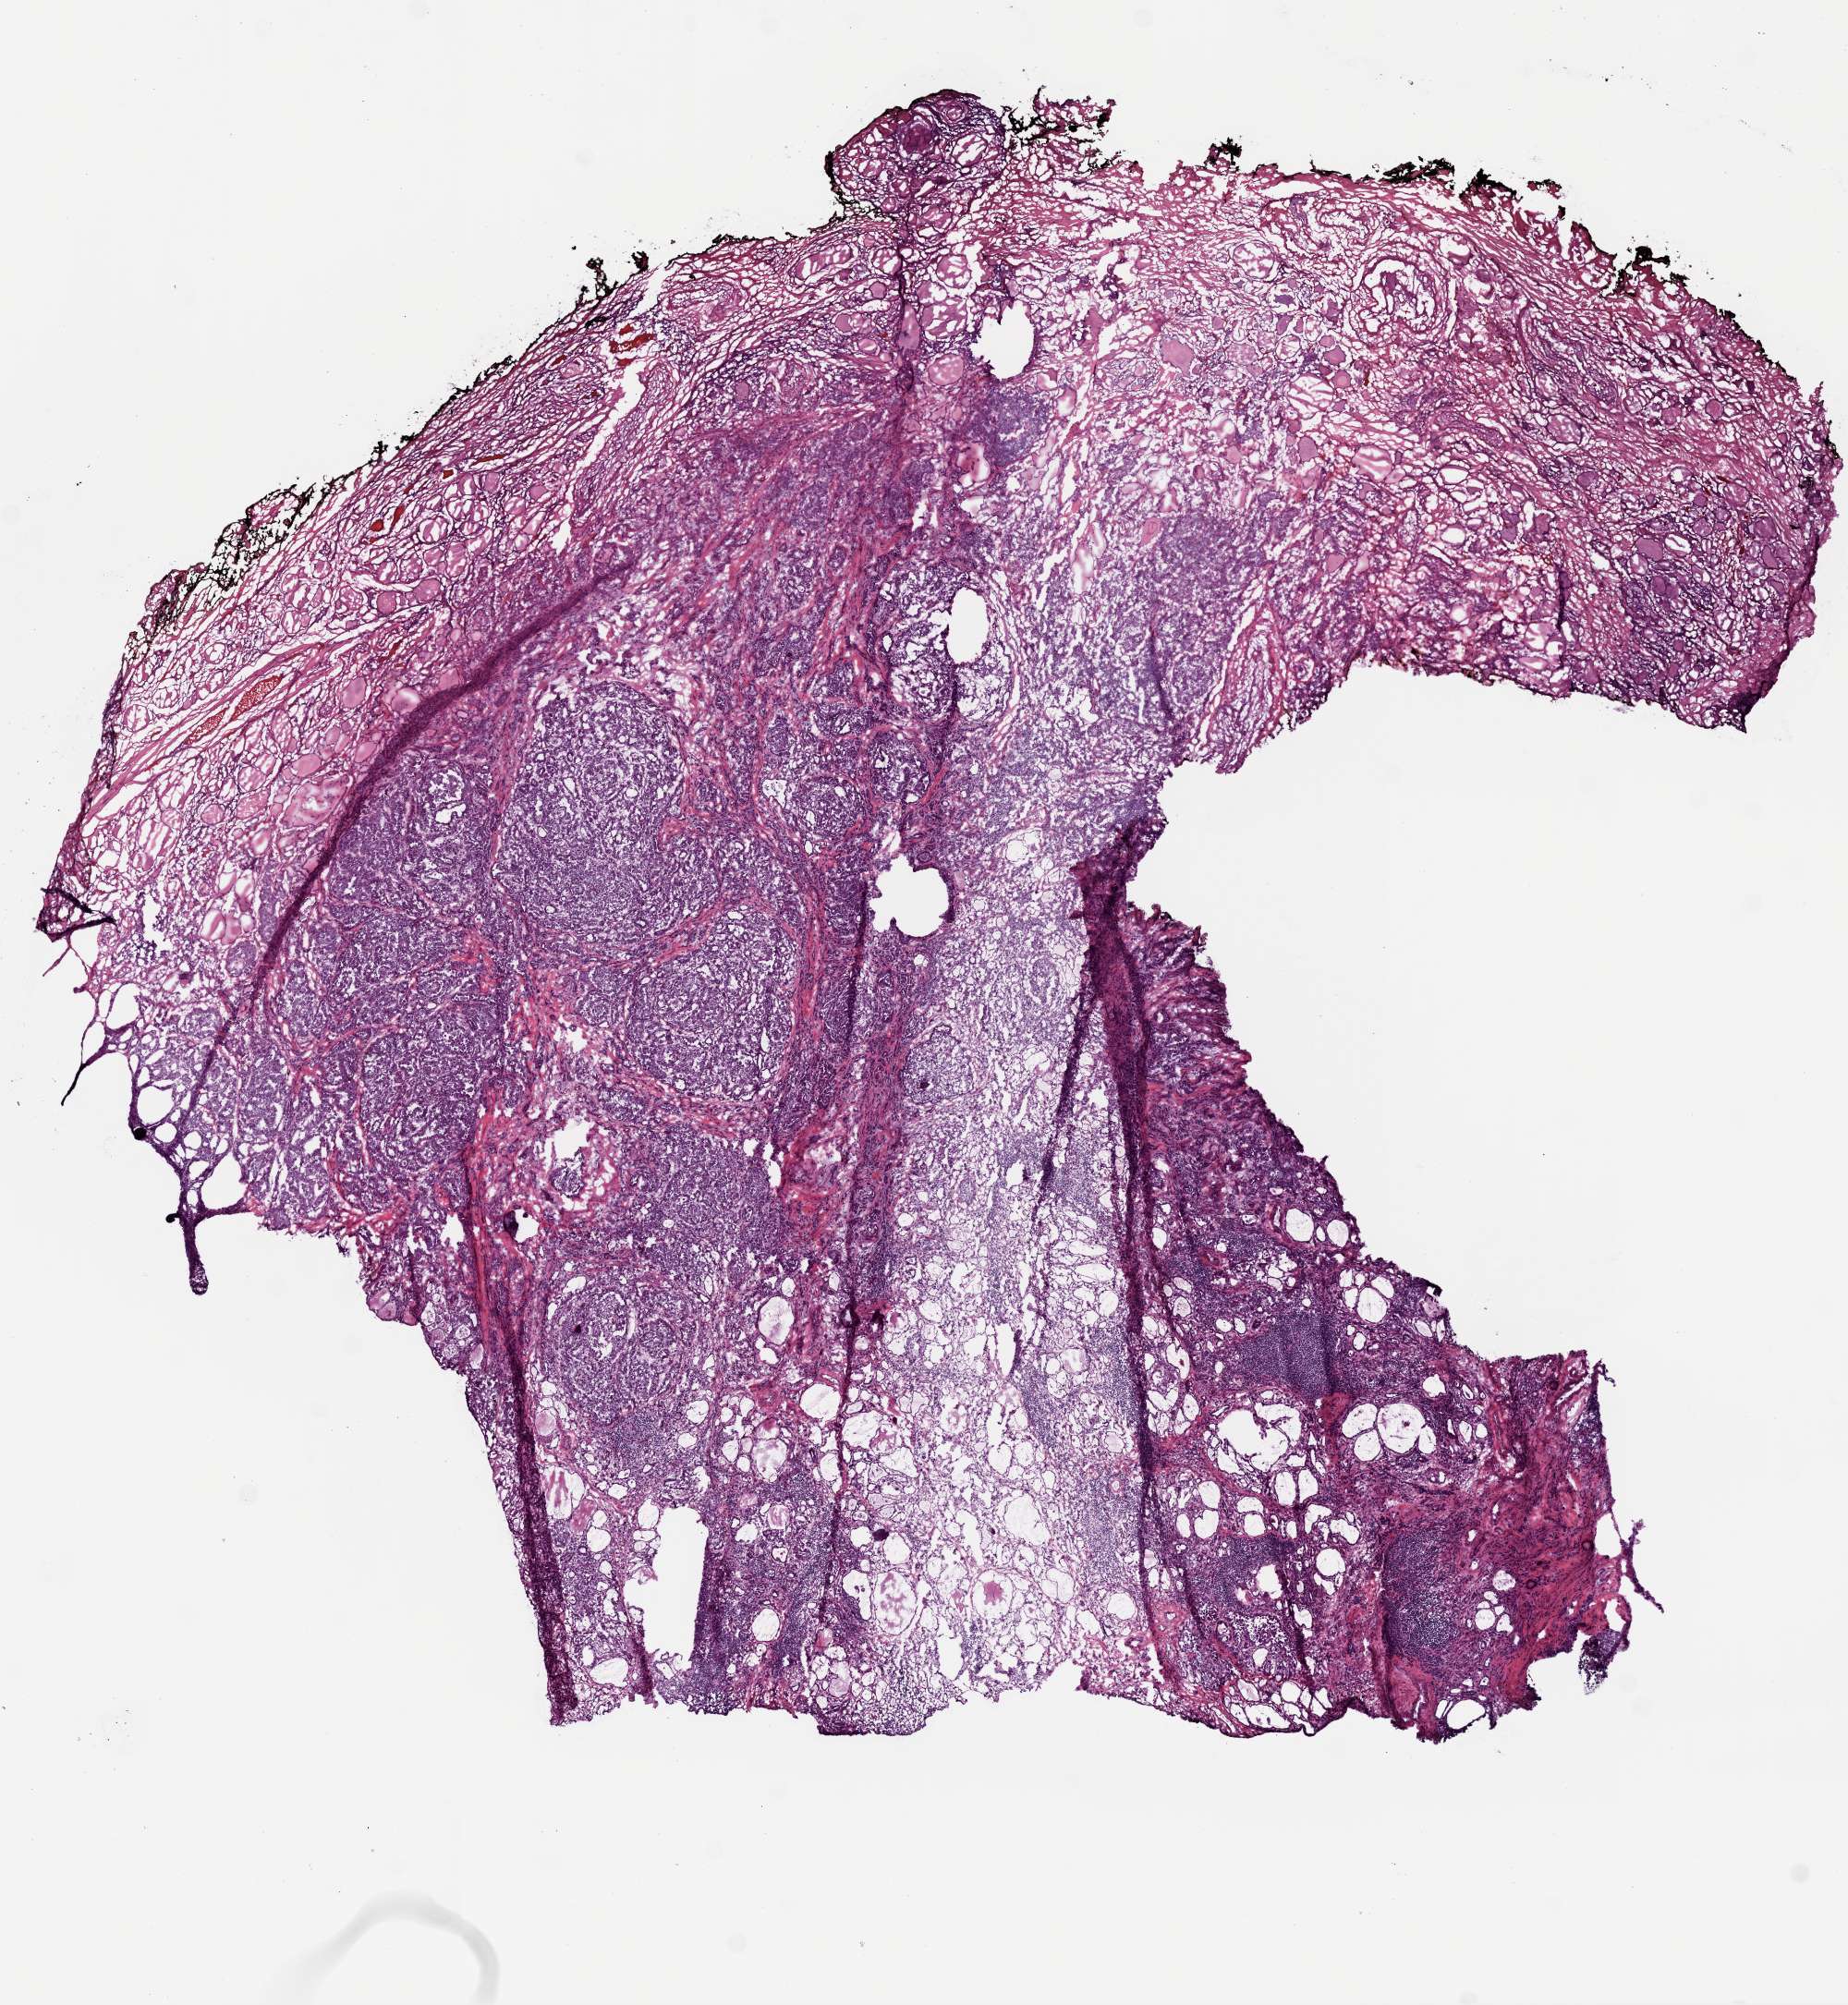
Whole-slide histology image, Hematoxylin and eosin (H&E) stained, a low-resolution overview of the entire scanned area, about 8.0 x 8.7 mm; frozen section from the top of the tissue portion; primary tumour sample from the thyroid. Female, age 57 years at initial diagnosis. Slide review estimates, as recorded: tumour cells 95%, tumour nuclei 80%, normal cells 0%, stromal cells 5%, necrosis 0%. Infiltration values recorded for this section: lymphocyte infiltration 0%, monocyte infiltration 0%, neutrophil infiltration 0%.
Laterality: left. Pathologic diagnosis: Papillary adenocarcinoma, NOS (thyroid gland). Lymph nodes positive (case pathology): 5 of 30 examined. AJCC pathologic stage: IVA (7th edition).